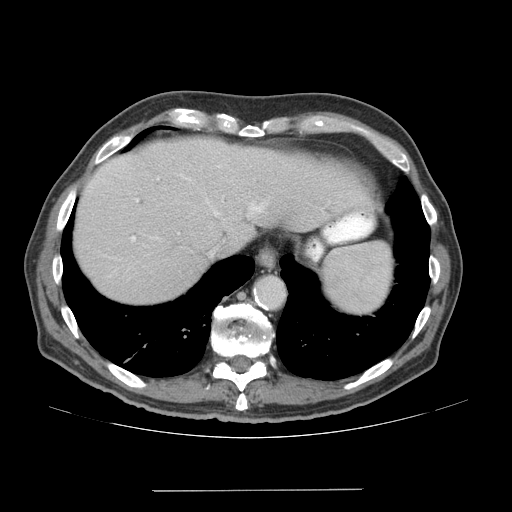
Contrast-enhanced abdominal CT (liver protocol), one axial slice; slice 58 of 77 in the series (ordered by position); soft-tissue window (W 400 / L 40 HU); 512 × 512 image matrix. Case-level facts recorded for this patient, not image findings: diagnosis: hepatocellular carcinoma (patient treated with transarterial chemoembolisation; whether this scan precedes or follows treatment is not stated here); TNM stage (as recorded): Stage-IVA; Child-Pugh class: A; tumour differentiation: well differentiated; tumour nodularity: uninodular.
Structures marked on this image (semi-automatic segmentation, software-assisted and operator-edited):
- abdominal aorta: bounding box [x1, y1, x2, y2] px = [257, 278, 285, 308]
- liver parenchyma outside the tumour (the mass and vessels are separate outlines, so this box may not span the whole liver): [74, 138, 372, 302]
- liver vessels: [107, 166, 264, 242]